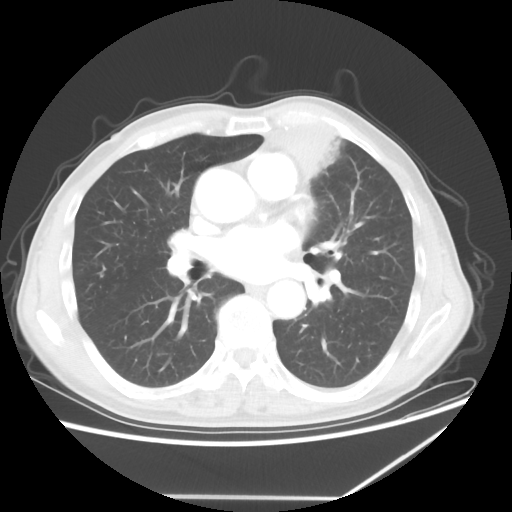
Chest CT, one axial slice. Slice 32 of 64 in the series (ordered by position). 100 kVp. Lung window (W 1500 / L -600 HU). 512 × 512 image matrix, field of view 383 × 383 mm. Patient: male, 64 years. Case-level facts recorded for this patient, not image findings: clinical TNM (as recorded): T1c N1 M1; histopathological grade: G2.
Outlined on this slice (rectangle marked by the reading radiologist):
- lung tumour (recorded histology: squamous cell carcinoma): box from (x=266, y=101) to (x=376, y=198) px